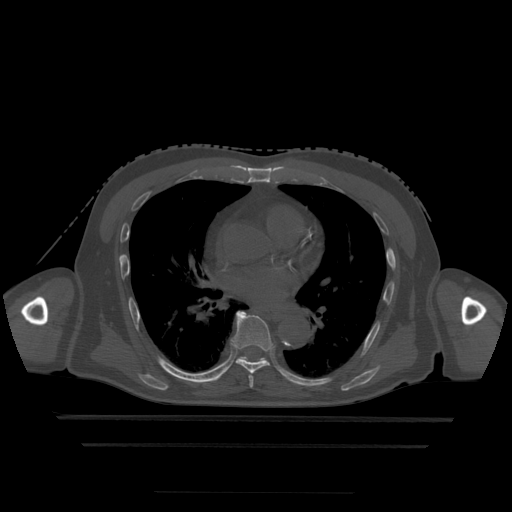
CT including the spine, one axial slice. Slice 297 of 522 in the series (ordered by position). Bone window (W 1800 / L 400 HU). 1.25 mm slice thickness. 512 × 512 image matrix, field of view 436 × 436 mm. Patient age 68 years. Case-level facts recorded for this patient, not image findings: primary cancer: urothelial.
Structures marked on this image (semi-automatic segmentation, software-assisted and operator-edited):
- T6 vertebra: bounding box [x1, y1, x2, y2] px = [249, 376, 254, 388]
- T7 vertebra: [231, 311, 274, 374]
- T8 vertebra: [239, 357, 267, 362]